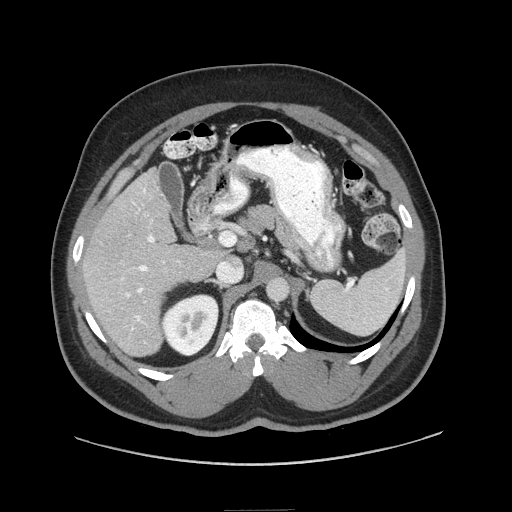
Contrast-enhanced abdominal CT (liver protocol), one axial slice. Position 43 of 87 along the scan axis. 140 kVp. Soft-tissue window (W 400 / L 40 HU). 2.5 mm slice thickness. 512 × 512 image matrix, field of view 440 × 440 mm. Case-level facts recorded for this patient, not image findings: diagnosis: hepatocellular carcinoma (patient treated with transarterial chemoembolisation; whether this scan precedes or follows treatment is not stated here); TNM stage (as recorded): Stage-II; Child-Pugh class: A; tumour differentiation: moderately differentiated; tumour nodularity: uninodular.
Structures marked on this image (semi-automatic segmentation, software-assisted and operator-edited):
- liver parenchyma outside the tumour (the mass and vessels are separate outlines, so this box may not span the whole liver): bounding box <82,168,222,356> (left, top, right, bottom; pixels)
- liver vessels: <120,188,179,331>